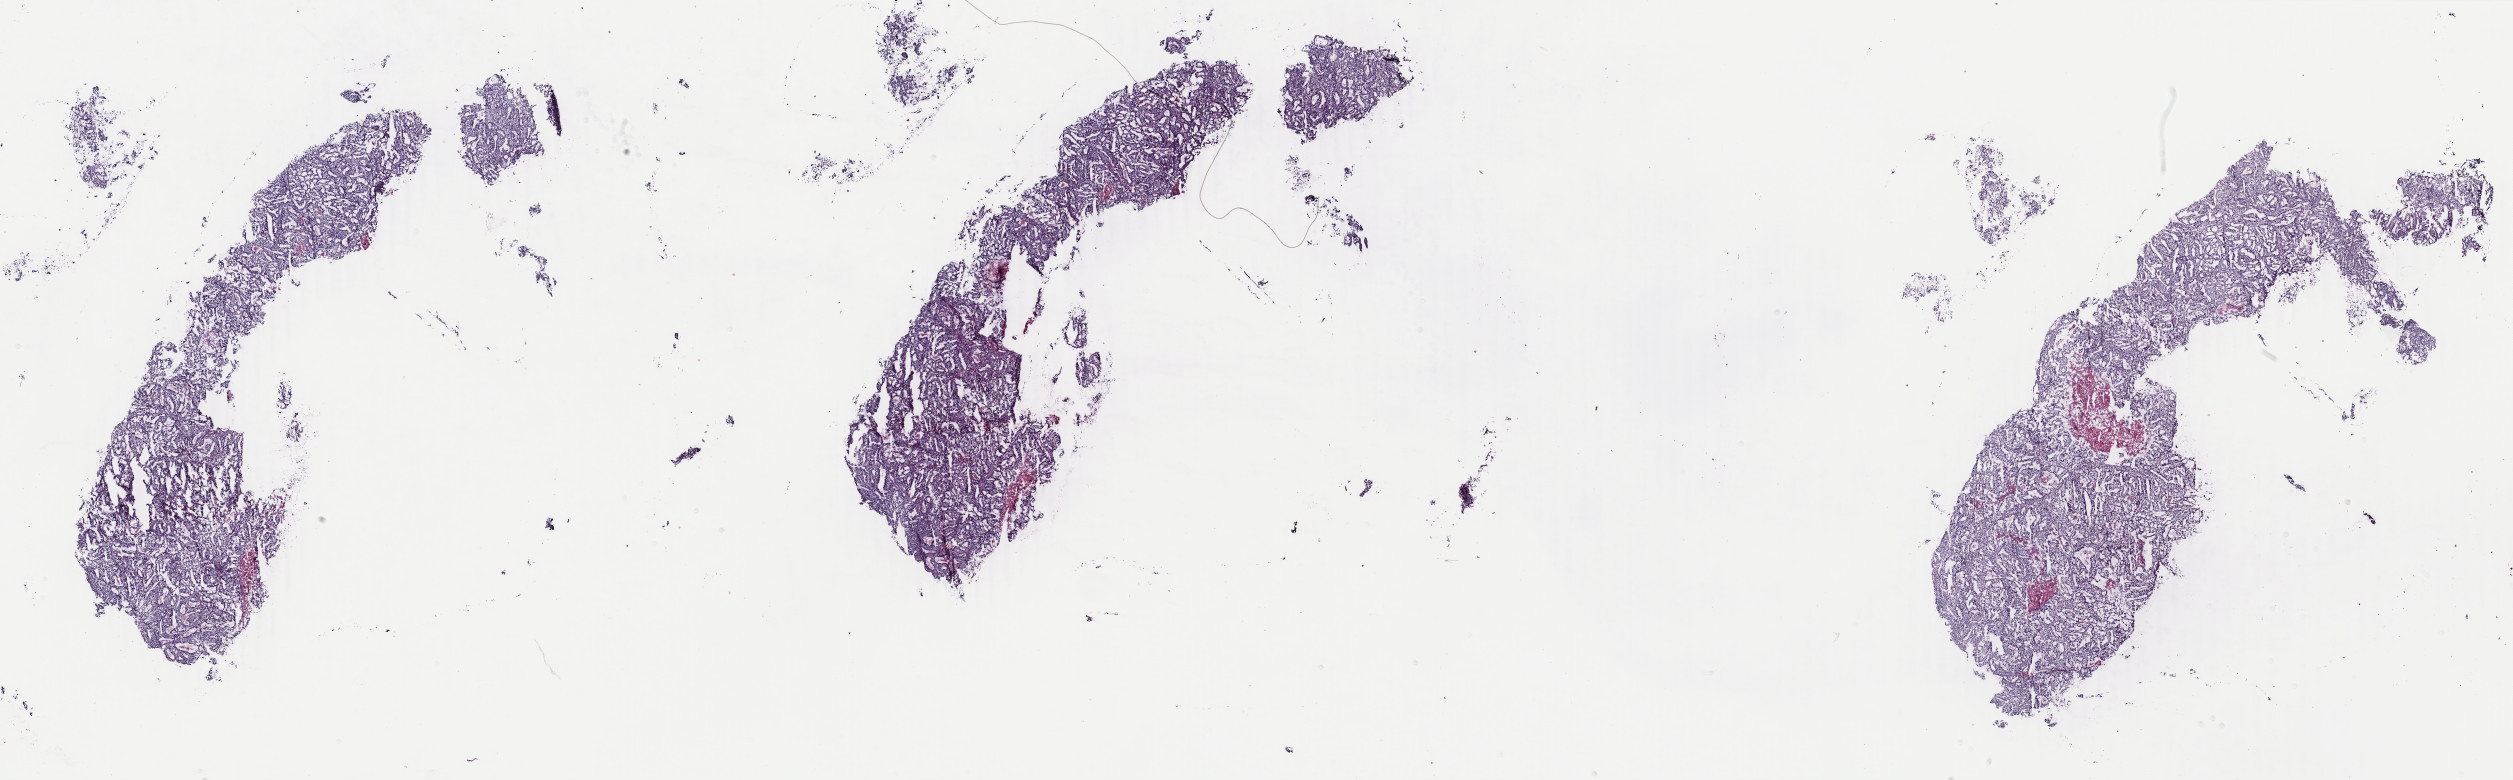
H&E-stained whole-slide image, shown as a low-resolution overview of the whole scanned area (about 40.0 x 12.4 mm, from a 40x scan). Frozen section from the bottom of the tissue portion. Primary tumour sample from the uterus. Patient: female, age at initial diagnosis 44 years. Histologic grade: G2 (moderately differentiated). Composition of this section per pathologist review: tumour cells 70%, tumour nuclei 100%, normal cells 0%, stromal cells 0%, necrosis 30%. Infiltration values recorded for this section: lymphocyte infiltration 10%, monocyte infiltration 0%, neutrophil infiltration 15%.
FIGO stage: IA. Lymph nodes positive (case pathology): 0 of 4 examined. Diagnosis: Endometrioid adenocarcinoma, NOS (endometrium).